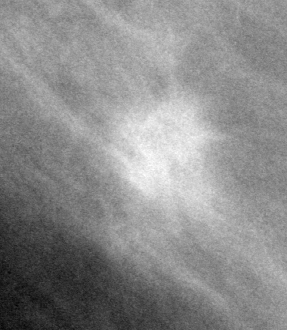
Crop from a digitized film mammogram around one marked abnormality; left breast; MLO view; BI-RADS breast density category 1 (scale 1–4).
Finding: mass, shape irregular, margins spiculated; BI-RADS assessment category 5; subtlety rating 5 on a 1 (subtle) to 5 (obvious) scale; pathology (as recorded): malignant.